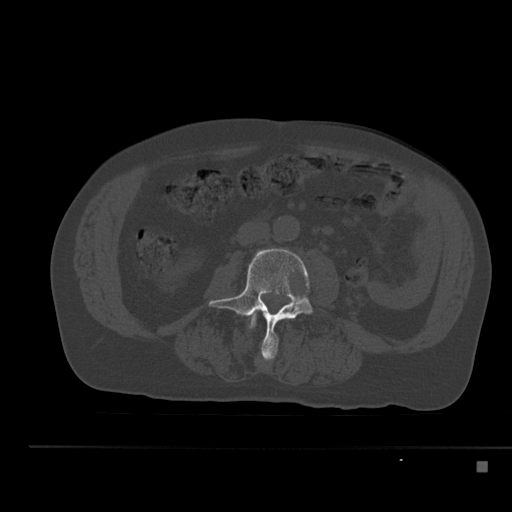
CT including the spine, one axial slice; position 165 of 517 along the scan axis; 120 kVp; bone window (W 1800 / L 400 HU); 1.5 mm slice thickness; 512 × 512 image matrix, field of view 408 × 408 mm. Patient: male, 70 years. Case-level facts recorded for this patient, not image findings: primary cancer: renal; vertebrae with lytic lesions (as recorded): T4, T6, T10, T12, L3, L4, L5.
Structures marked on this image (semi-automatically segmented with operator editing):
- L2 vertebra: bounding box <249,313,291,337> (left, top, right, bottom; pixels)
- L3 vertebra: <208,248,314,361>